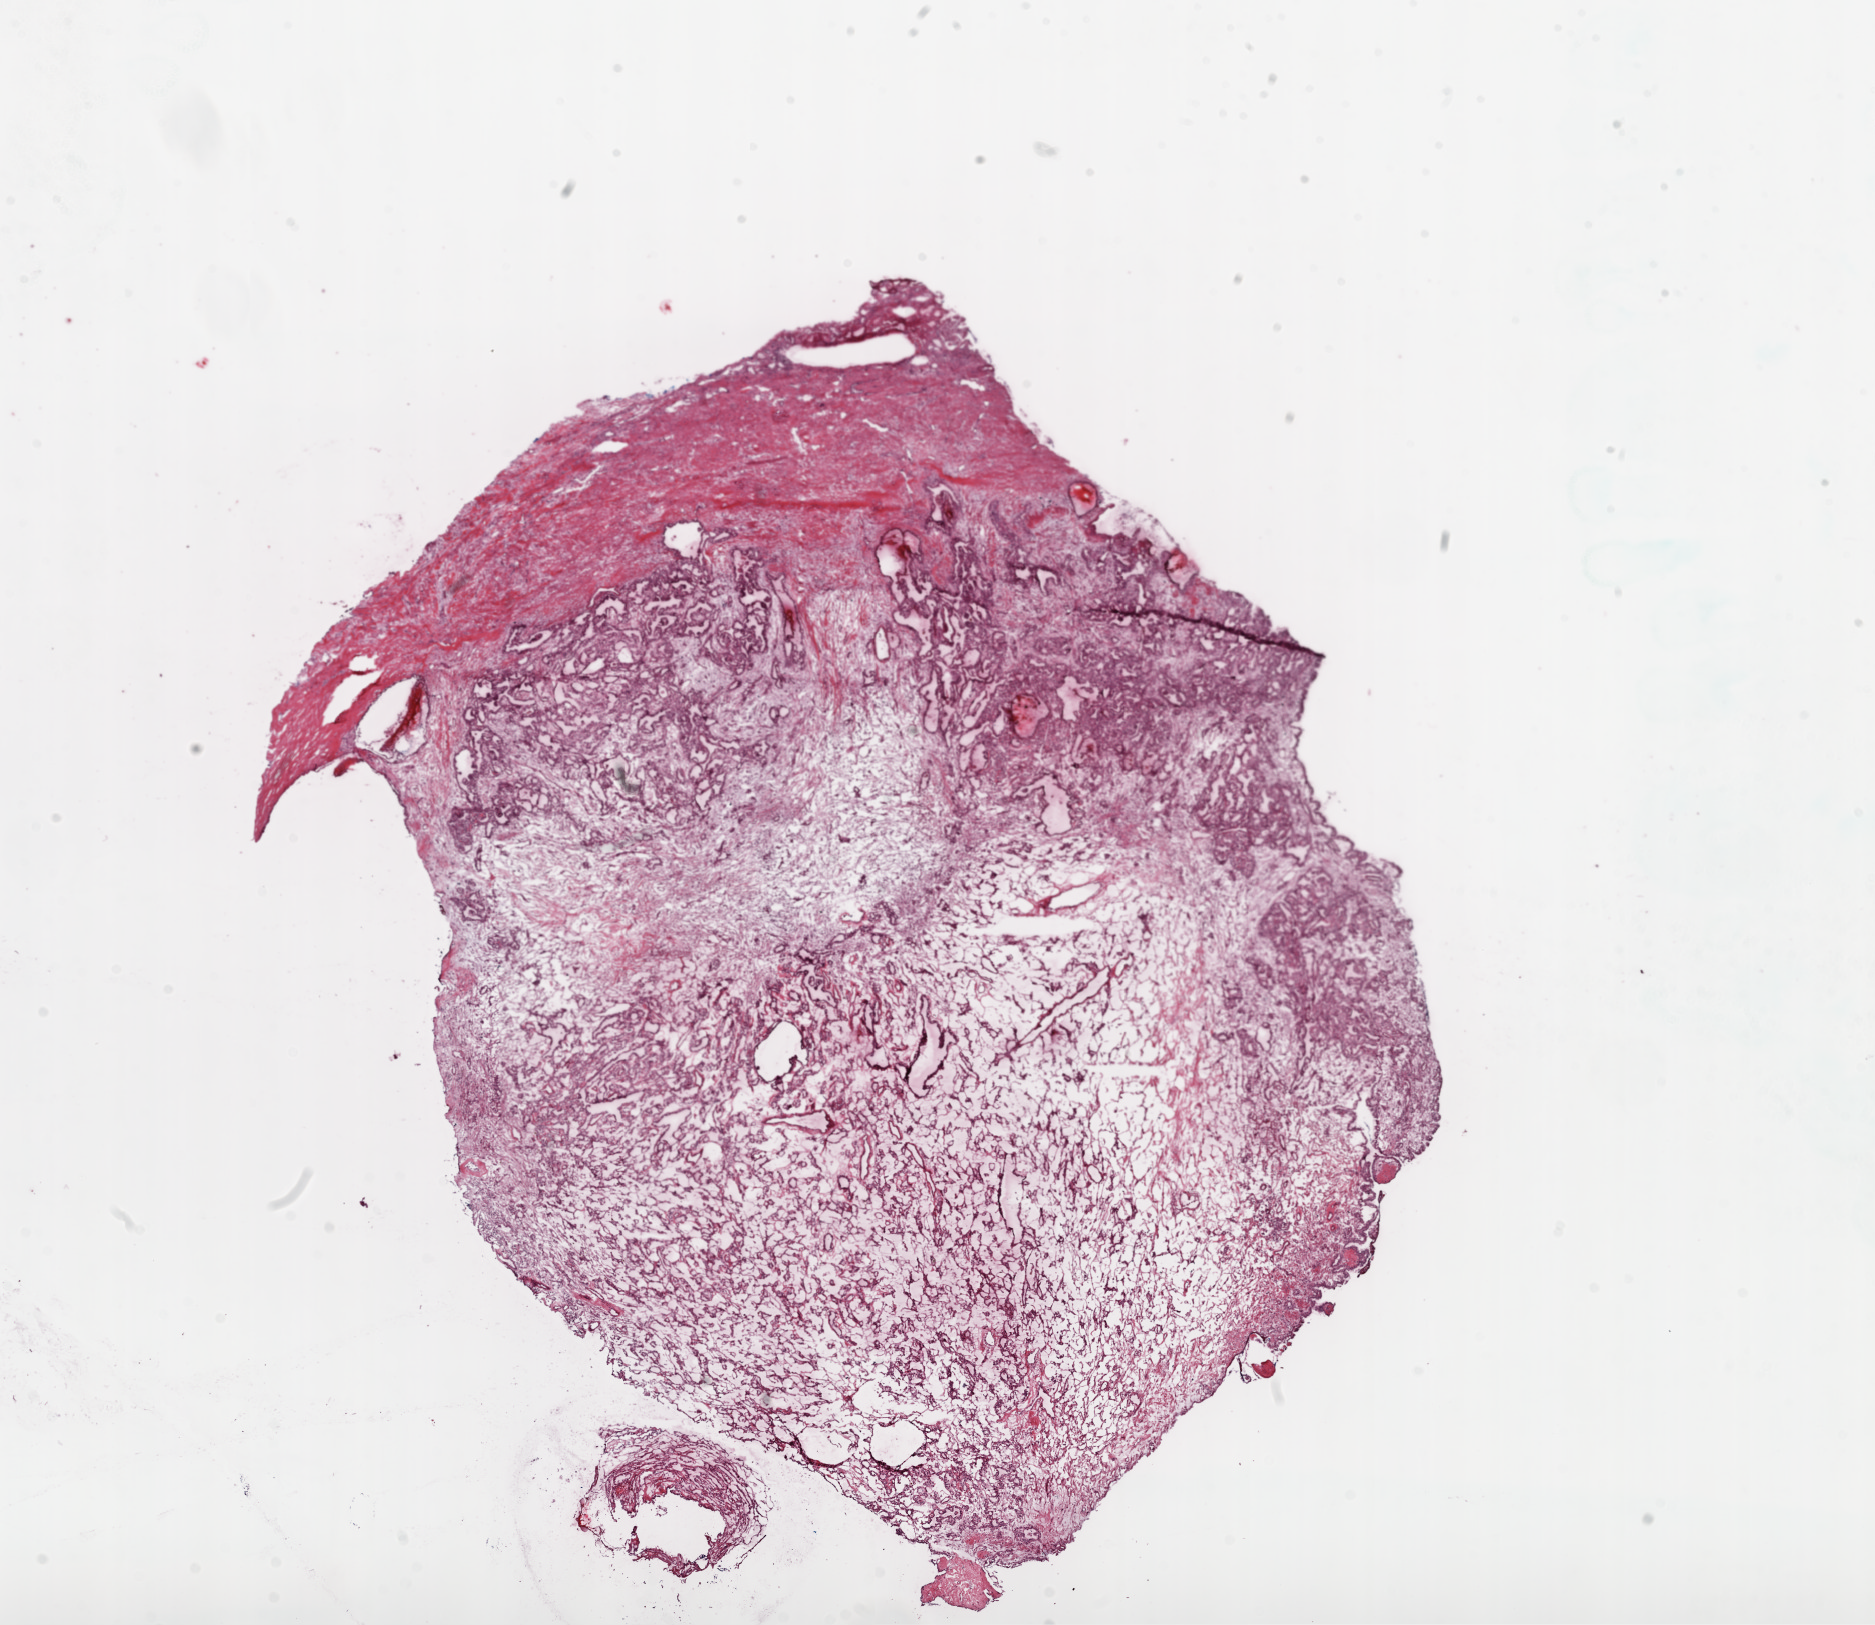
Digitized Hematoxylin and eosin (H&E) stained tissue section (whole slide) — whole scanned area (about 15.0 x 13.0 mm) shown as a low-resolution overview; frozen section; sample: primary tumour, kidney. Female patient; age at initial diagnosis 67 years. Histologic grade: G2 (moderately differentiated). Pathologist review of this section (percent, as recorded): tumour cells 80%, tumour nuclei 85%, normal cells 0%, stromal cells 20%, necrosis 0%.
Histologic diagnosis: Clear cell adenocarcinoma, NOS. TNM: T1a NX M0. AJCC pathologic stage: I. Laterality: right.